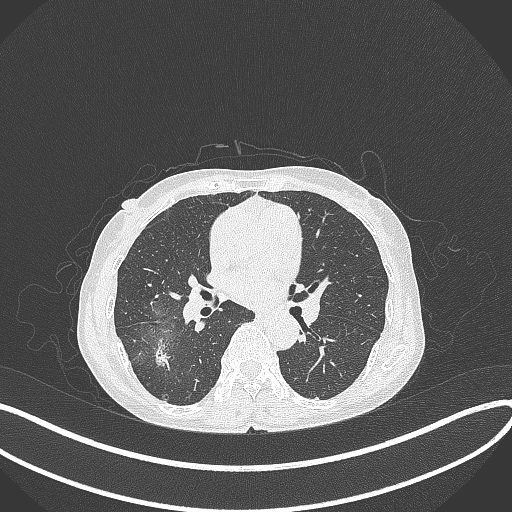
Chest CT, one axial slice; position 206 of 371 along the scan axis; 120 kVp; lung window (W 1500 / L -600 HU); 1 mm slice thickness; 512 × 512 image matrix, field of view 400 × 400 mm. Patient: female, 69 years. From the clinical record (not read from this slice): clinical TNM (as recorded): T1b N0 M0; histopathological grade: G2-3.
Structures marked on this image (bounding box drawn by a radiologist):
- lung tumour (recorded histology: adenocarcinoma): bounding box [x1, y1, x2, y2] px = [149, 337, 180, 375]